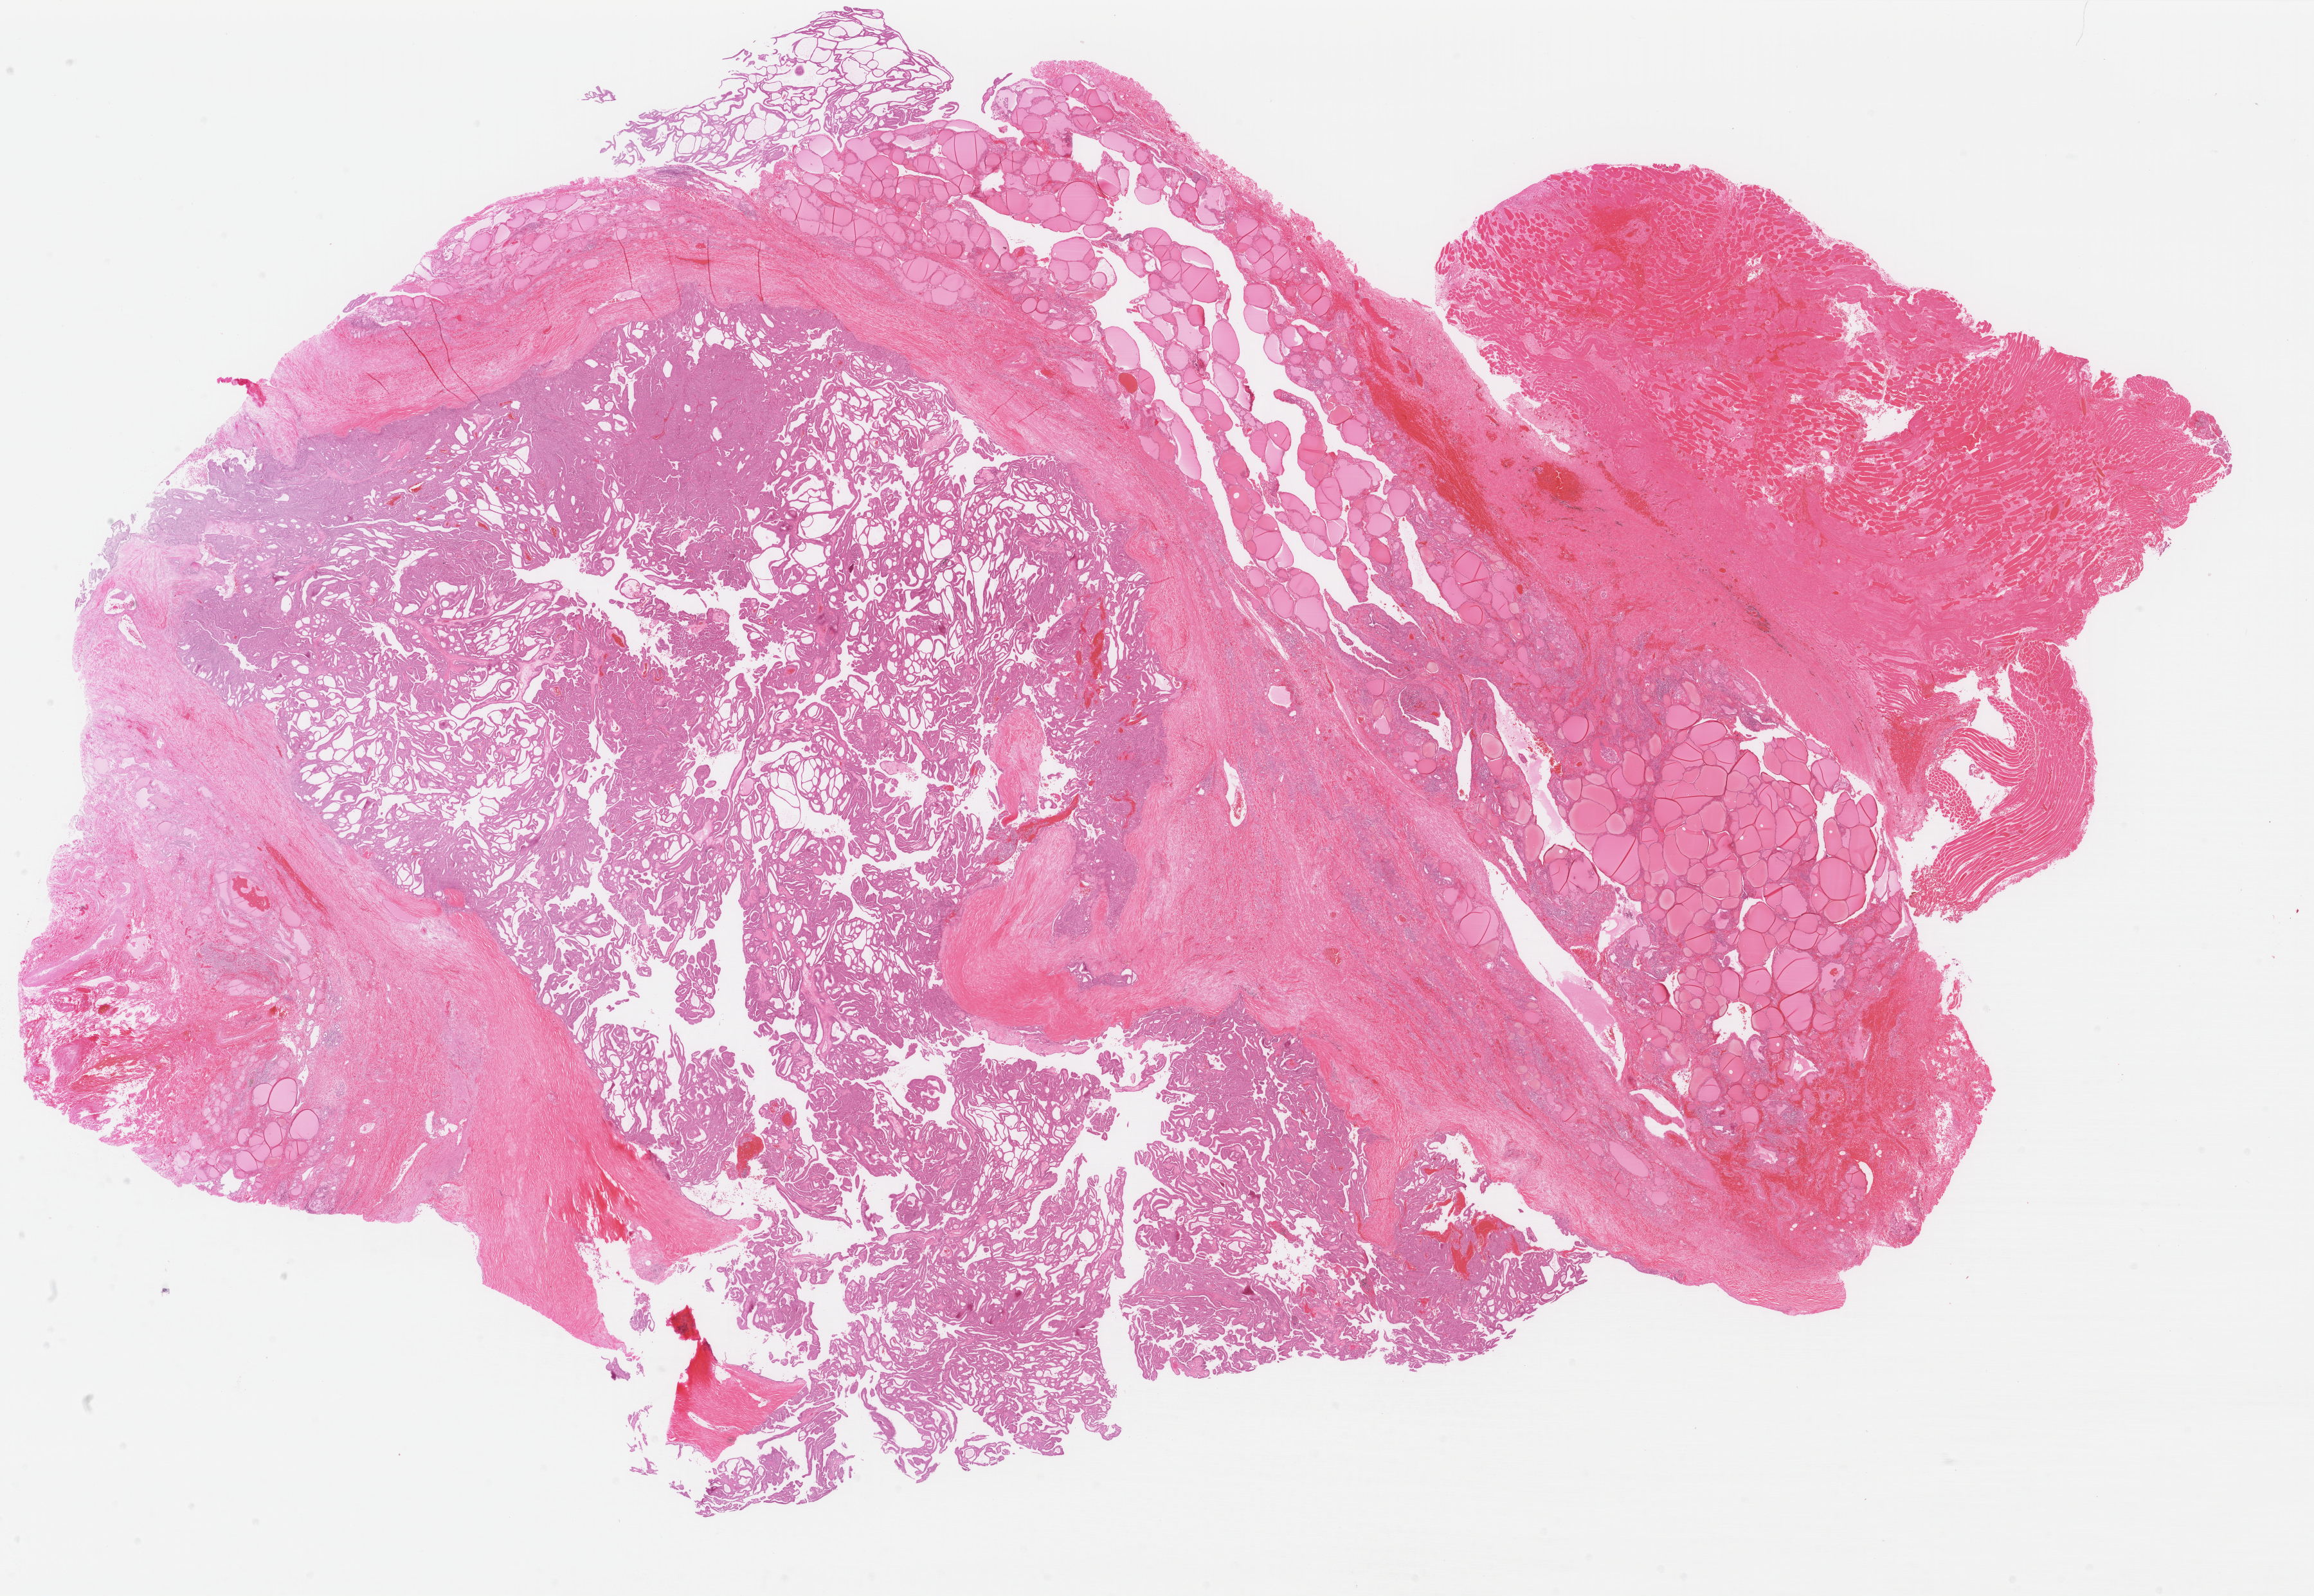
Digitized H&E-stained tissue section (whole slide), shown as a low-resolution overview of the whole scanned area (about 28.6 x 19.7 mm, acquisition: 40x scan), formalin-fixed paraffin-embedded (FFPE) diagnostic section, primary tumour sample from the thyroid. Patient: female, age at initial diagnosis 22 years.
Laterality: right. AJCC pathologic stage: I (6th edition). Histologic diagnosis: Papillary adenocarcinoma, NOS (thyroid gland). Lymph nodes positive (case pathology): 0 of 13 examined.